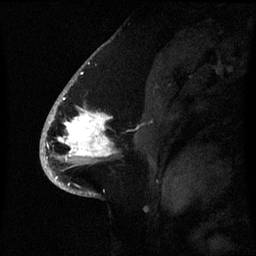
Breast MRI (dynamic contrast-enhanced), one sagittal slice; slice 40 of 60 in the series (ordered by position); dynamic contrast-enhanced series, image 2 of 3 at this slice position (ordered by acquisition); 1.5 T; TE 4.2 ms, TR 8.4 ms; 2.1 mm slice thickness; 256 × 256 image matrix, field of view 220 × 220 mm. Patient: female, 53 years. From the clinical record (not read from this slice): setting: breast cancer imaged before/during neoadjuvant chemotherapy; receptor status: HR-positive, HER2-negative.
Structures marked on this image (semi-automatic segmentation, software-assisted and operator-edited):
- analysis volume of interest (the breast-tissue region the enhancement analysis was run in; not a lesion): bounding box <52,90,115,171> (left, top, right, bottom; pixels)
- tumour enhancement mask (voxels above the 70 % enhancement threshold inside the analysis volume of interest): <58,102,113,161>